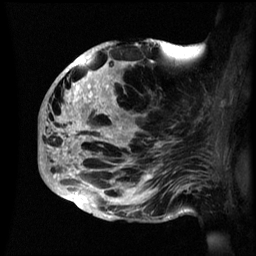
Breast MRI (dynamic contrast-enhanced), one sagittal slice; slice 29 of 60 in the series (ordered by position); dynamic contrast-enhanced series, image 2 of 3 at this slice position (ordered by acquisition); 1.5 T; TE 4.2 ms, TR 8.4 ms; 2.4 mm slice thickness; 256 × 256 image matrix. Female patient, age 48 years.
Structures marked on this image (semi-automatic segmentation, software-assisted and operator-edited):
- analysis volume of interest (the breast-tissue region the enhancement analysis was run in; not a lesion): box from (x=40, y=41) to (x=195, y=222) px
- tumour enhancement mask (voxels above the 70 % enhancement threshold inside the analysis volume of interest): (x=40, y=45)–(x=177, y=214)